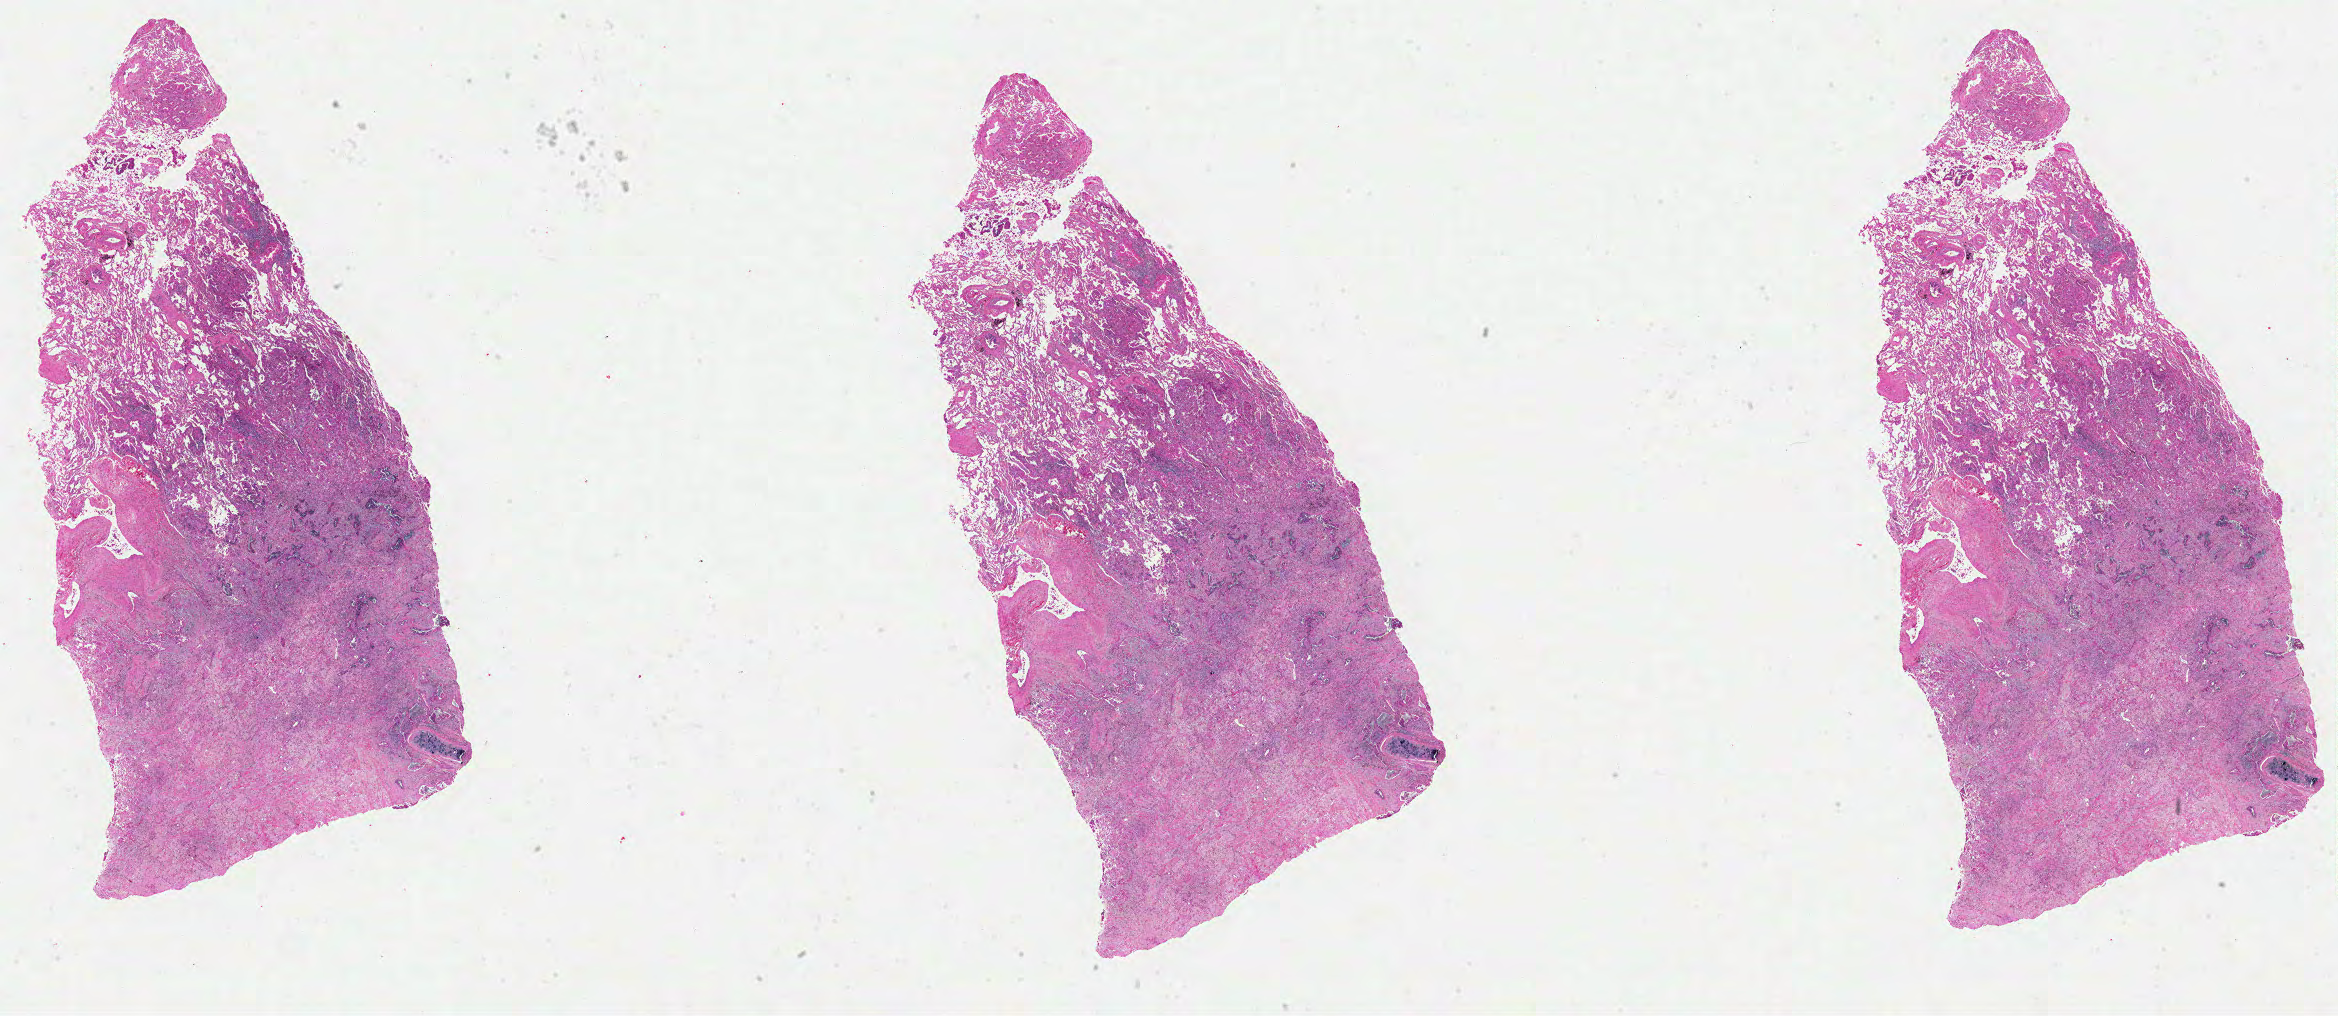
Digitized H&E tissue section (whole slide) — shown as a low-resolution overview of the whole scanned area (about 37.7 x 16.4 mm, from a 40x scan). Formalin-fixed paraffin-embedded (FFPE) diagnostic section. Lung, primary tumour sample. Female patient; age at initial diagnosis 64 years.
Pathologic diagnosis: Adenocarcinoma, NOS (upper lobe, lung).